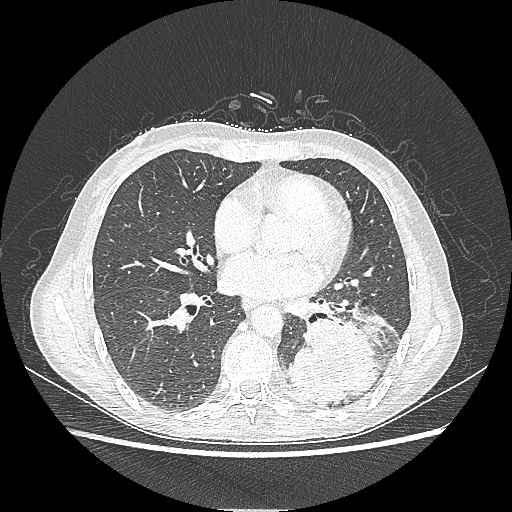
Chest CT, one axial slice. Position 101 of 220 along the scan axis. Lung window (W 1500 / L -600 HU). 1.25 mm slice thickness. 512 × 512 image matrix, field of view 360 × 360 mm. Female patient, age 53 years. Case-level facts recorded for this patient, not image findings: clinical TNM (as recorded): T3 N0 M0.
Structures marked on this image (bounding box drawn by a radiologist):
- lung tumour (recorded histology: adenocarcinoma): bounding box [x1, y1, x2, y2] px = [287, 315, 380, 407]